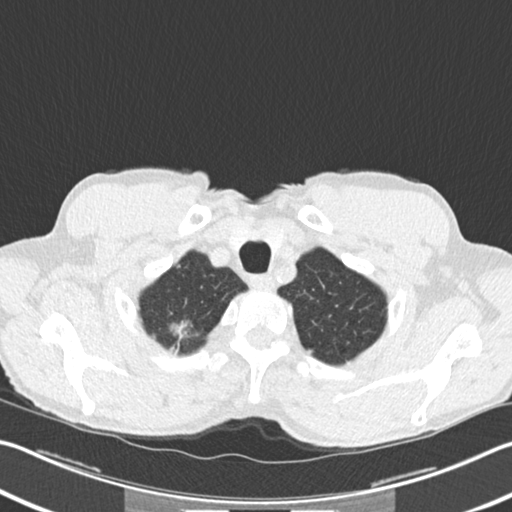
Low-dose screening chest CT, one axial slice. Slice 203 of 220 in the series (ordered by position). Reconstruction kernel B30f. Lung window (W 1500 / L -600 HU). 512 × 512 image matrix, field of view 342 × 342 mm.
Structures marked on this image (expert manual segmentation):
- lesion 1 (tumor, upper lobe of right lung): box from (x=172, y=322) to (x=188, y=334) px